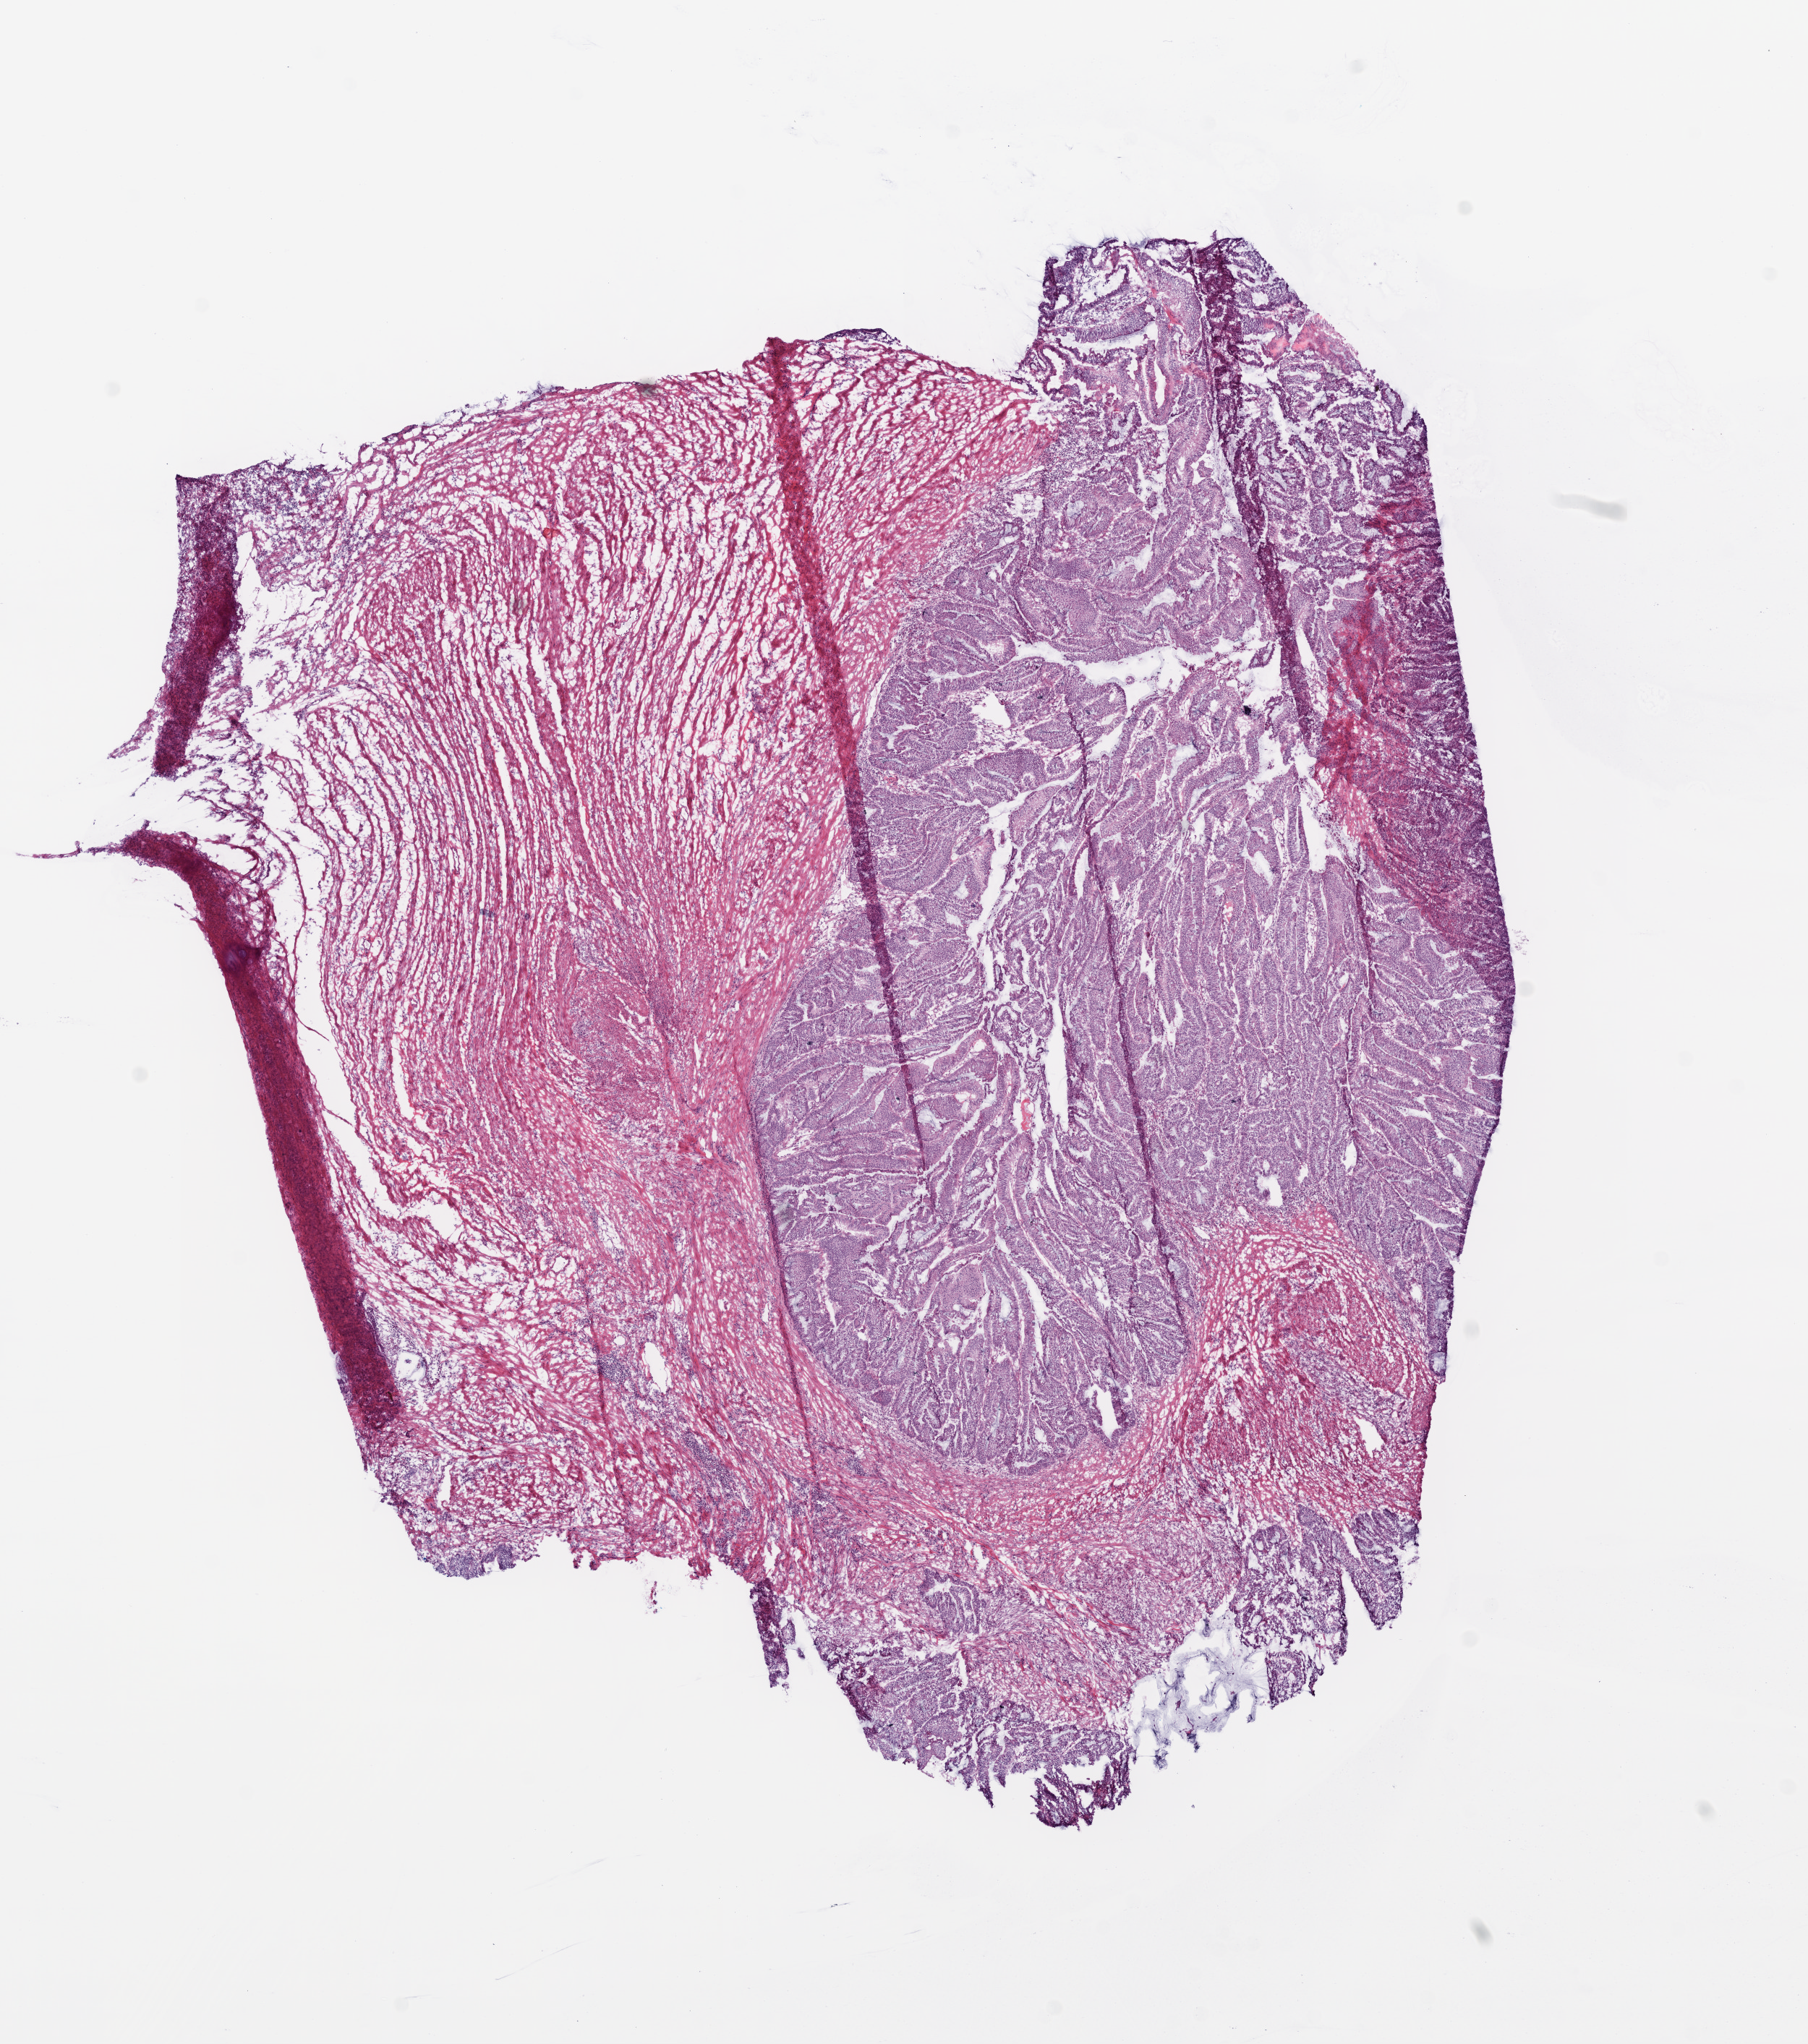
Whole-slide histology image, H&E-stained — shown as a low-resolution overview of the whole scanned area (about 10.0 x 11.3 mm, slide scanned at 20x); frozen section from the bottom of the tissue portion; sample: primary tumour, colon. Female patient; age at initial diagnosis 78 years.
Pathologic diagnosis: Adenocarcinoma, NOS.